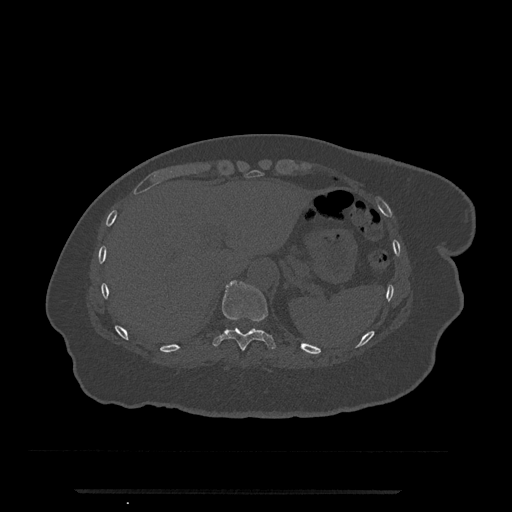
CT including the spine, one axial slice; position 280 of 797 along the scan axis; 120 kVp; bone window (W 1800 / L 400 HU); 0.5 mm slice thickness; 512 × 512 image matrix, field of view 440 × 440 mm. Female patient, age 51 years. From the clinical record (not read from this slice): primary cancer: neuro; vertebrae with lytic lesions (as recorded): T8.
Outlined on this slice (semi-automatically segmented with operator editing):
- T10 vertebra: bounding box (x1, y1, x2, y2) in pixels: (212, 281, 276, 351)